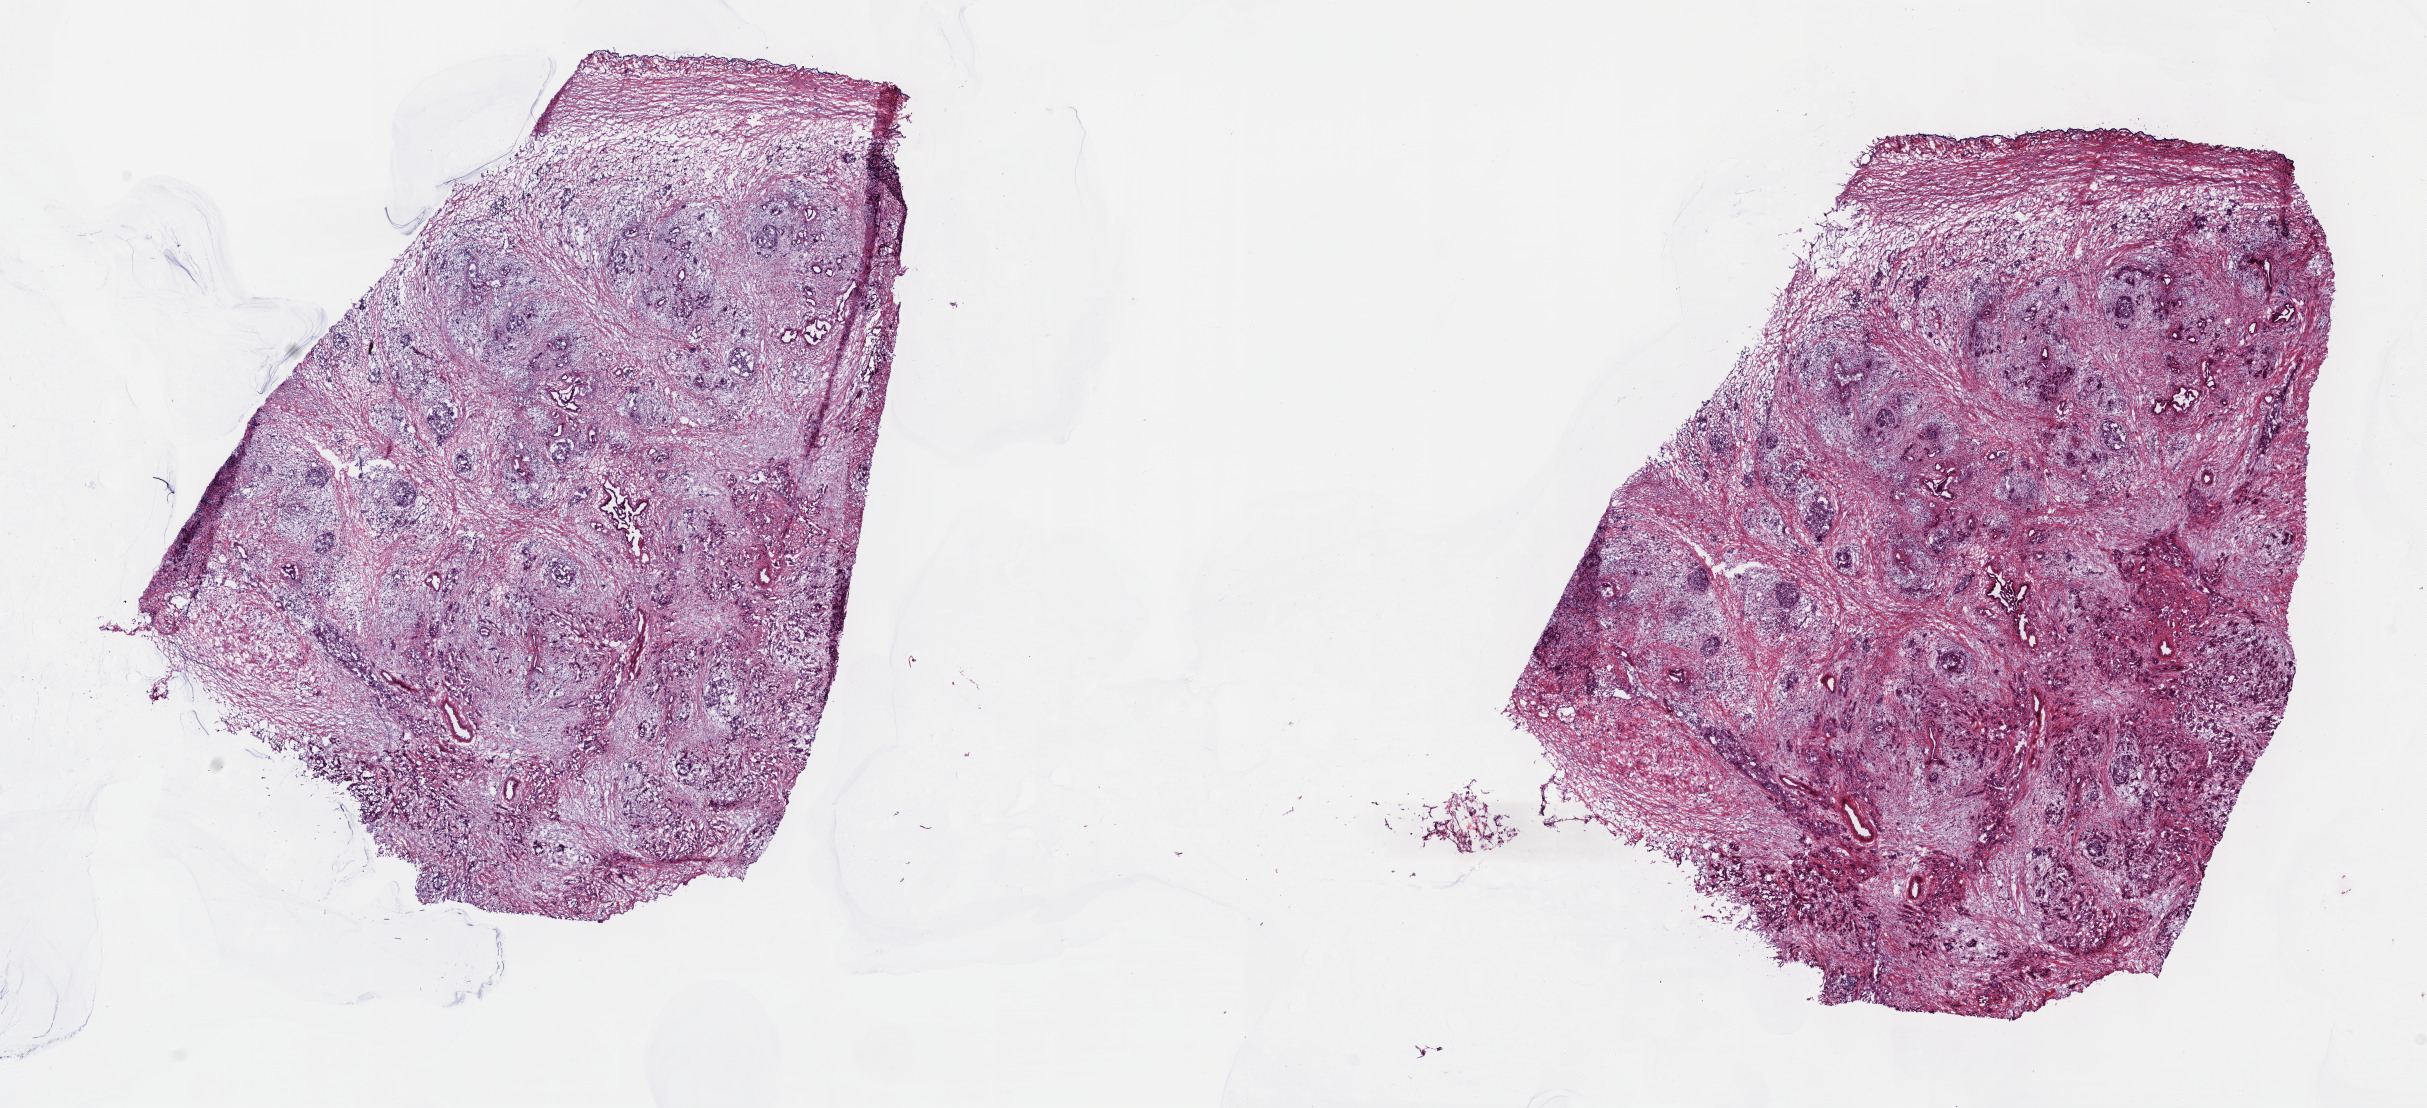
Hematoxylin and eosin (H&E) stained whole-slide image — shown as a low-resolution overview of the whole scanned area (about 19.6 x 9.0 mm). Frozen section. Pancreas, primary tumour sample. Patient: male, age at initial diagnosis 43 years. Histologic grade: G3 (poorly differentiated). Composition of this section per pathologist review: tumour cells 22%, tumour nuclei 85%, normal cells 4%, stromal cells 72%, necrosis 2%. Inflammatory infiltration, as recorded: lymphocyte infiltration 8%, monocyte infiltration 1%, neutrophil infiltration 1%.
Diagnosis: Infiltrating duct carcinoma, NOS (tail of pancreas). TNM: T1 N1 MX. Lymph nodes positive (case pathology): 1 of 9 examined. AJCC pathologic stage: IIB (7th edition).